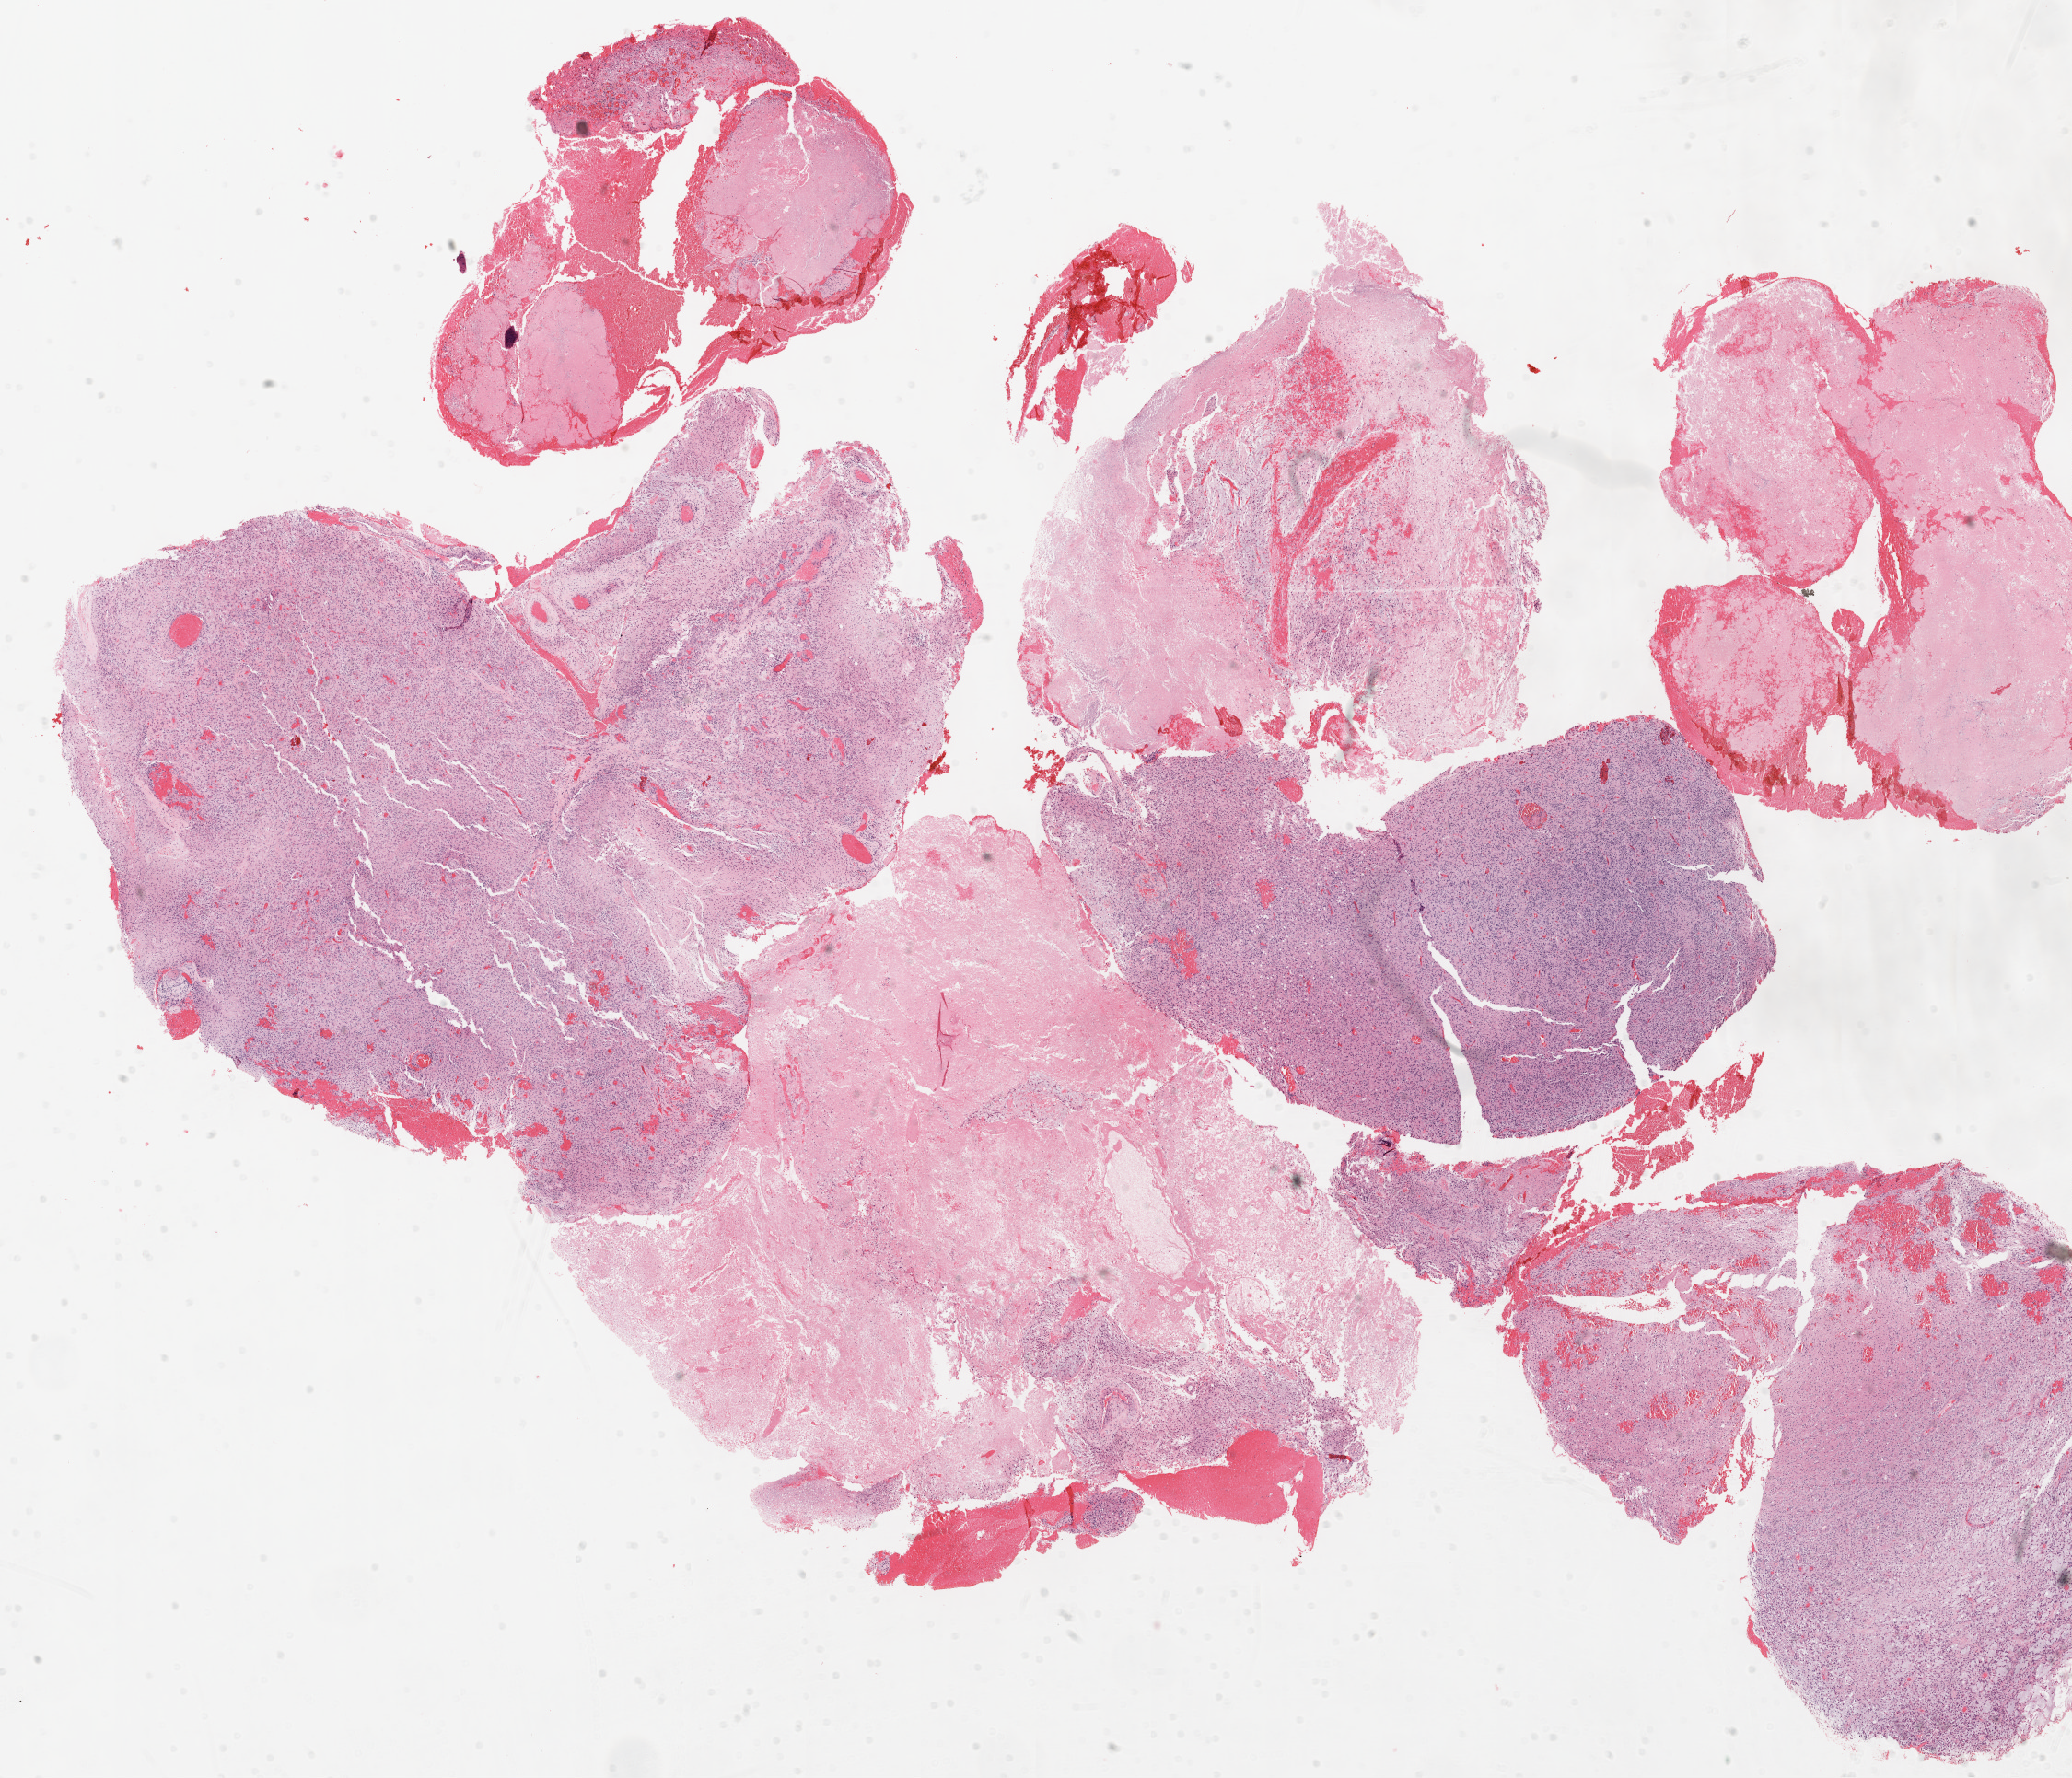
Whole-slide histology image, Hematoxylin and eosin (H&E) stained — a low-resolution overview of the entire scanned area, about 18.1 x 15.5 mm (from a 20x scan). Formalin-fixed paraffin-embedded (FFPE) diagnostic section. Primary tumour sample from the brain. Patient: male, age at initial diagnosis 54 years.
Pathologic diagnosis: Glioblastoma.